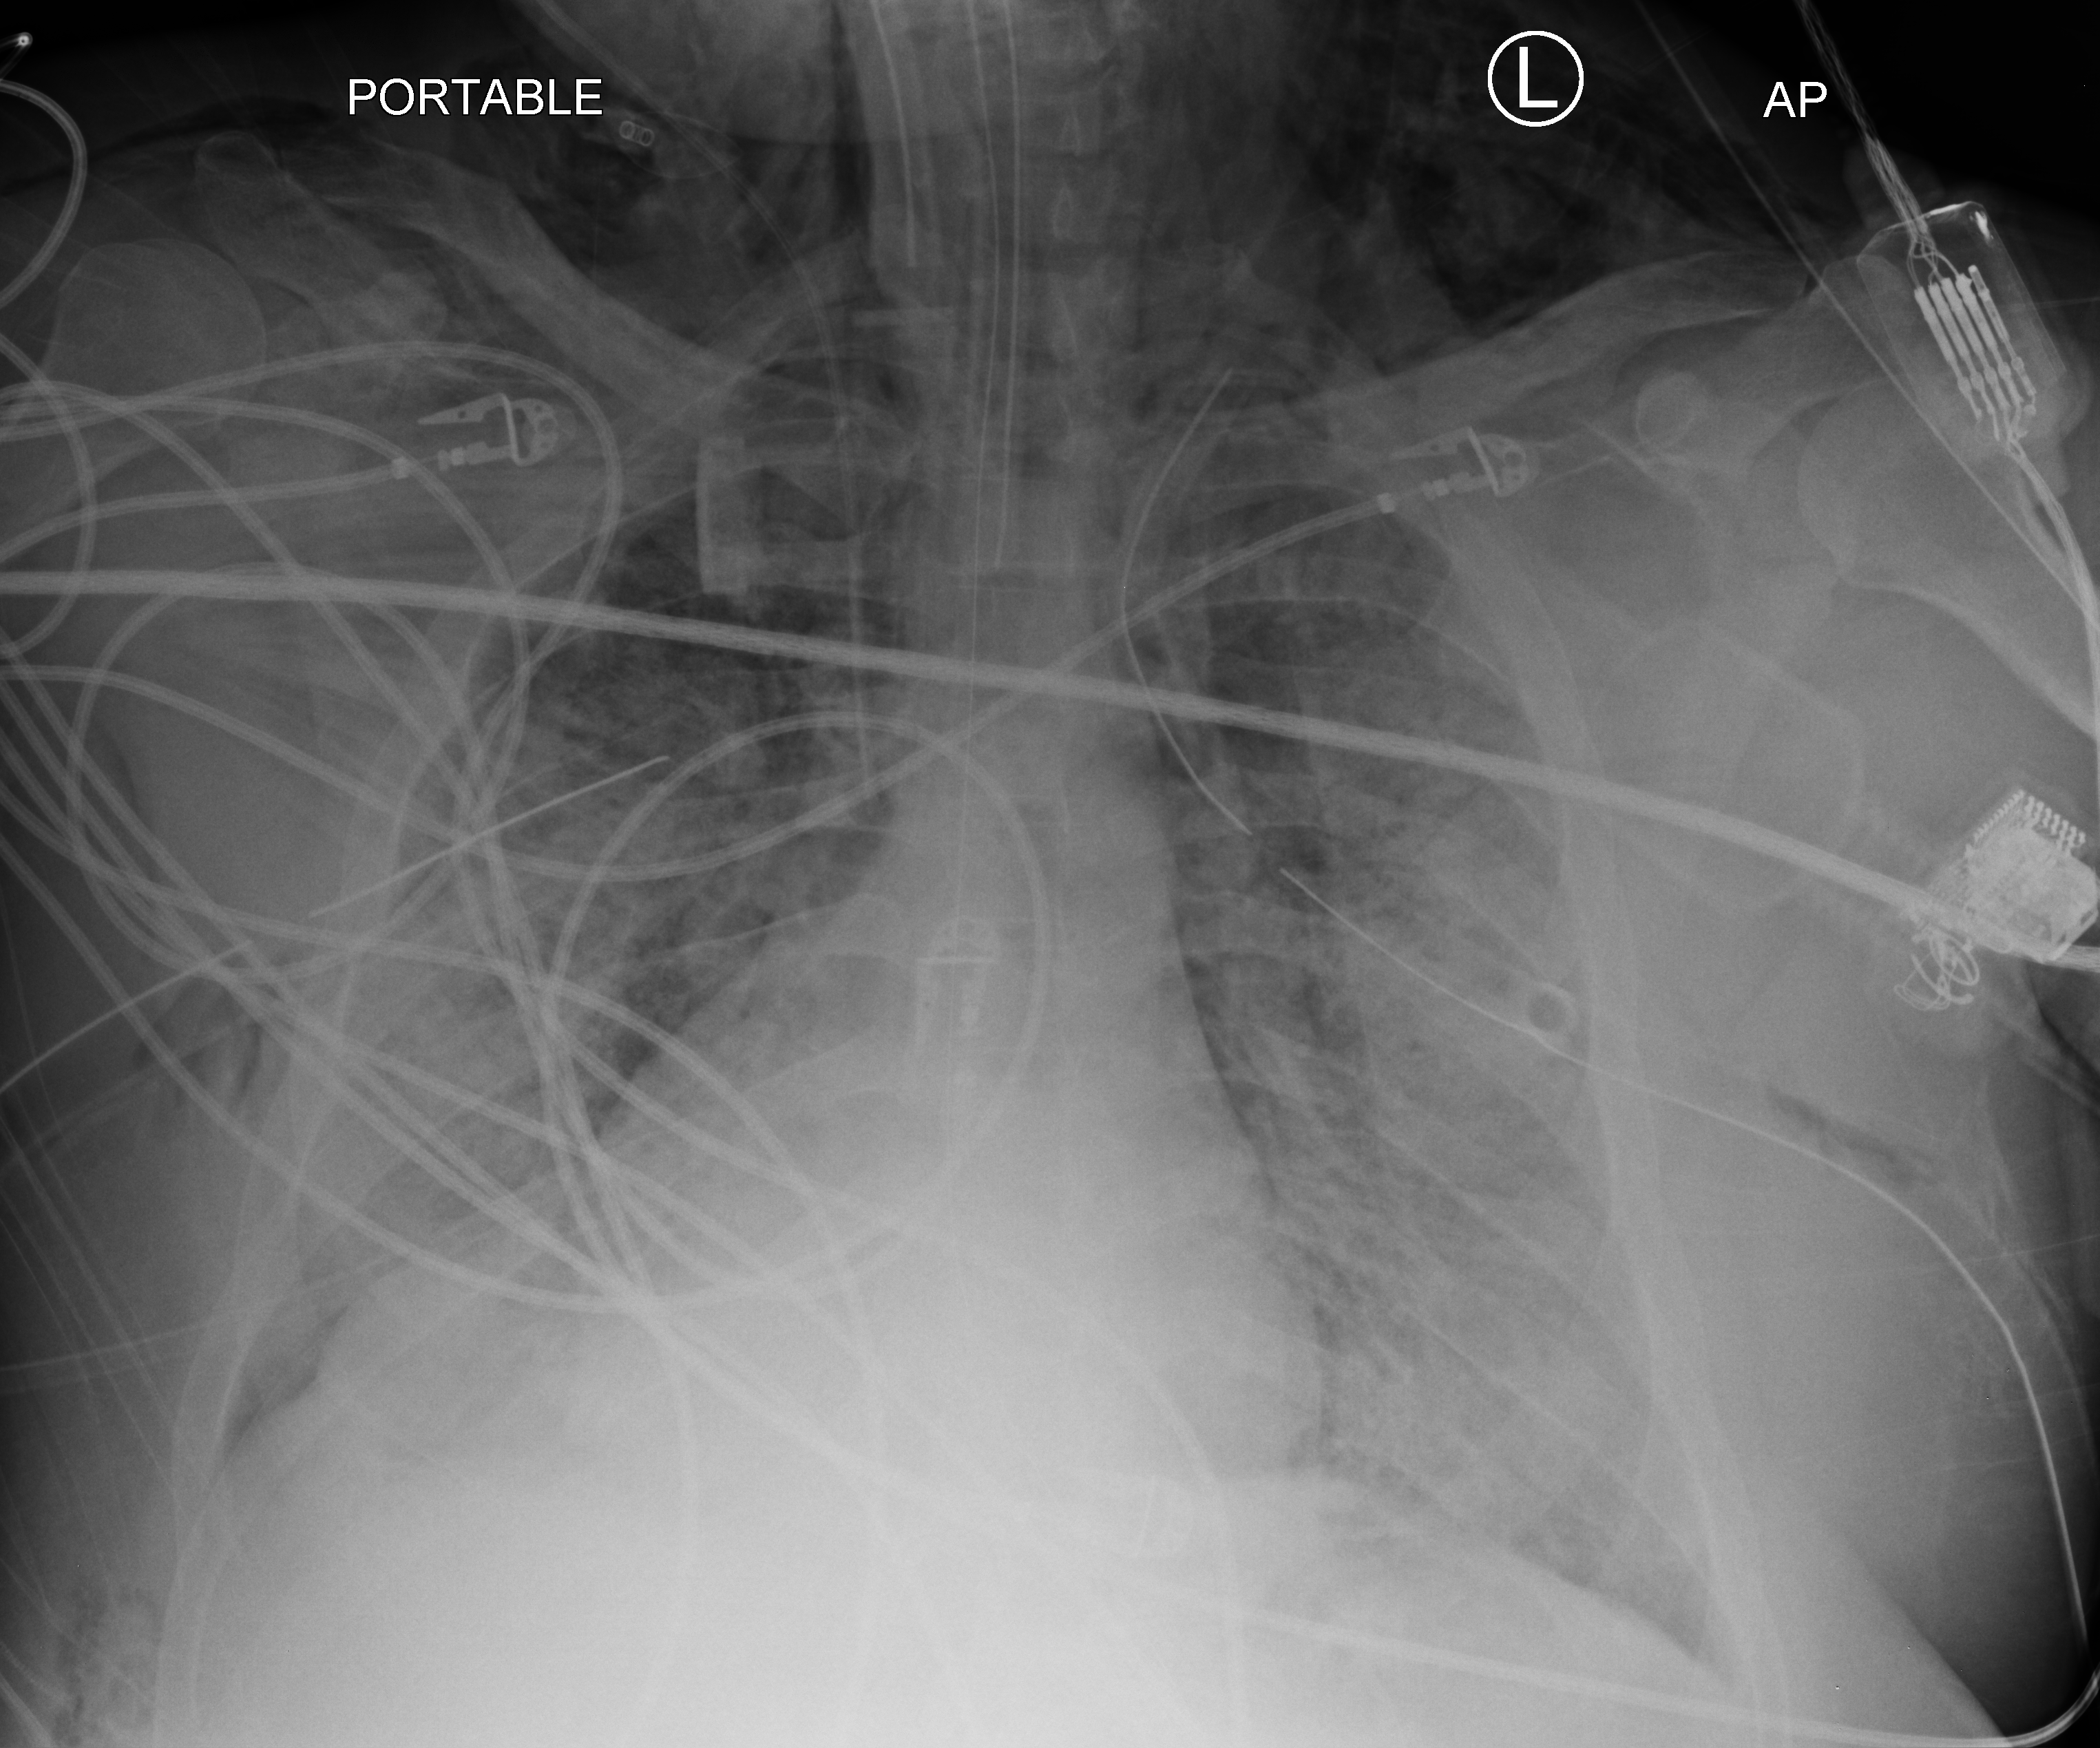
Bedside chest radiograph (computed radiography); anteroposterior (AP) projection. Patient hospitalised with COVID-19, aged 18–59 years.
From the hospital-stay record, not from the radiograph (when in the stay this image was taken is not recorded): chronic kidney disease (admission record): no; admitted to intensive care during this hospital stay: yes; mechanically ventilated during this hospital stay: yes.